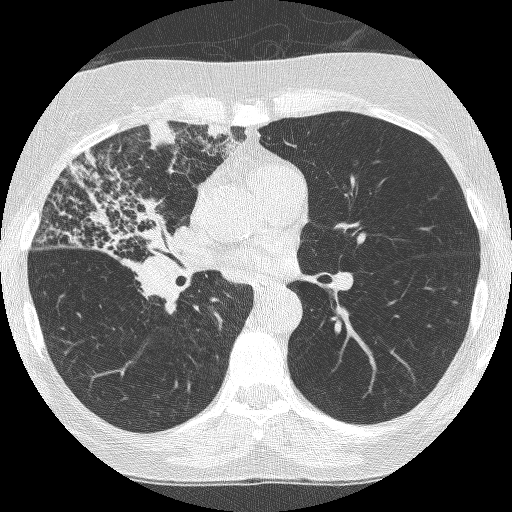
Chest CT (low-dose screening protocol), one axial image. Third annual screen. Lung window (W 1500 / L -600 HU). 120 kVp. Slice 139 of 253 in the series. 512 × 512 image matrix, field of view 294 × 294 mm. Female participant, aged 64 years at enrolment. Former smoker at enrolment.
Expert reader's lesion annotation, bounding box [x1, y1, x2, y2] px = [61, 171, 201, 313]. Screening reader's record for this exam (one nodule recorded; not confirmed to be the boxed lesion): non-calcified nodule or mass ≥4 mm, right upper lobe, 49 × 43 mm, spiculated (stellate) margins, soft tissue attenuation, pre-existing on the prior screen: yes; interval growth: yes. Later outcome: lung cancer diagnosed 7 days after this screen — adenocarcinoma, NOS, right upper lobe, right middle lobe, right hilum, stage IV (AJCC 6th edition), 85 mm at pathology.